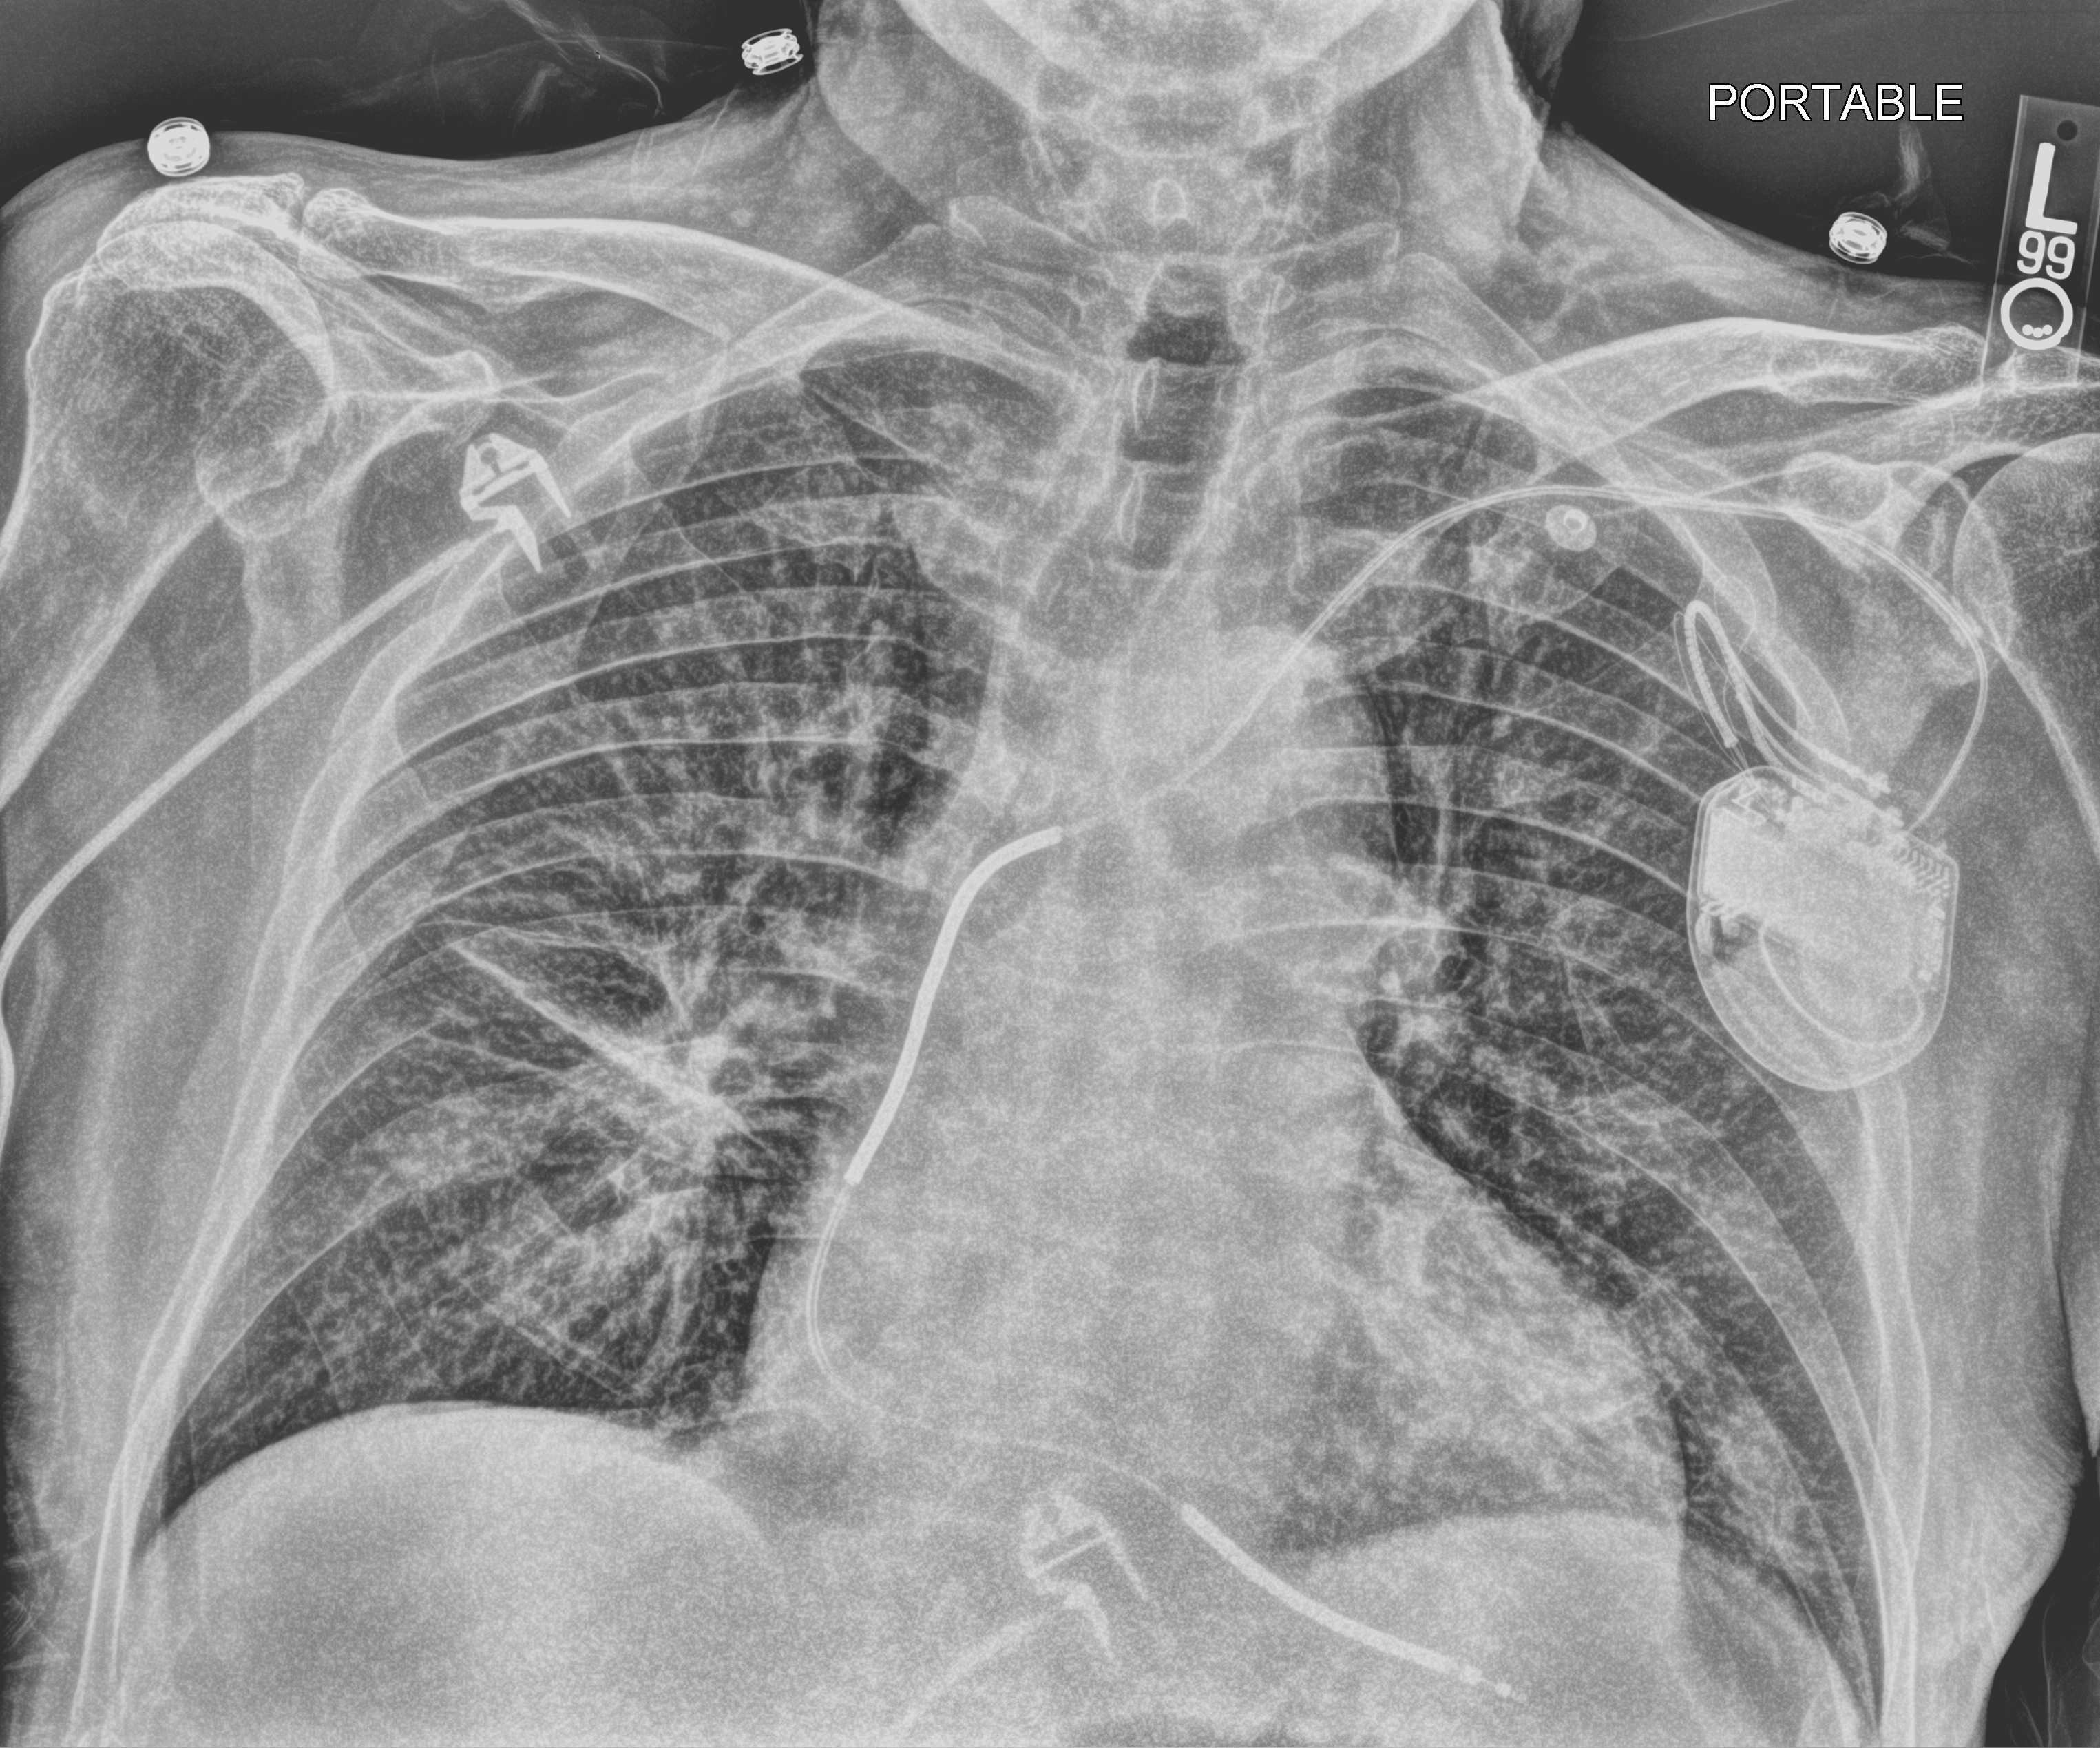
Portable chest radiograph; anteroposterior (AP) projection. Male patient hospitalised with COVID-19, age 75–90 years.
From the hospital-stay record, not from the radiograph (when in the stay this image was taken is not recorded):
- mechanically ventilated during this hospital stay: no
- admitted to intensive care during this hospital stay: no